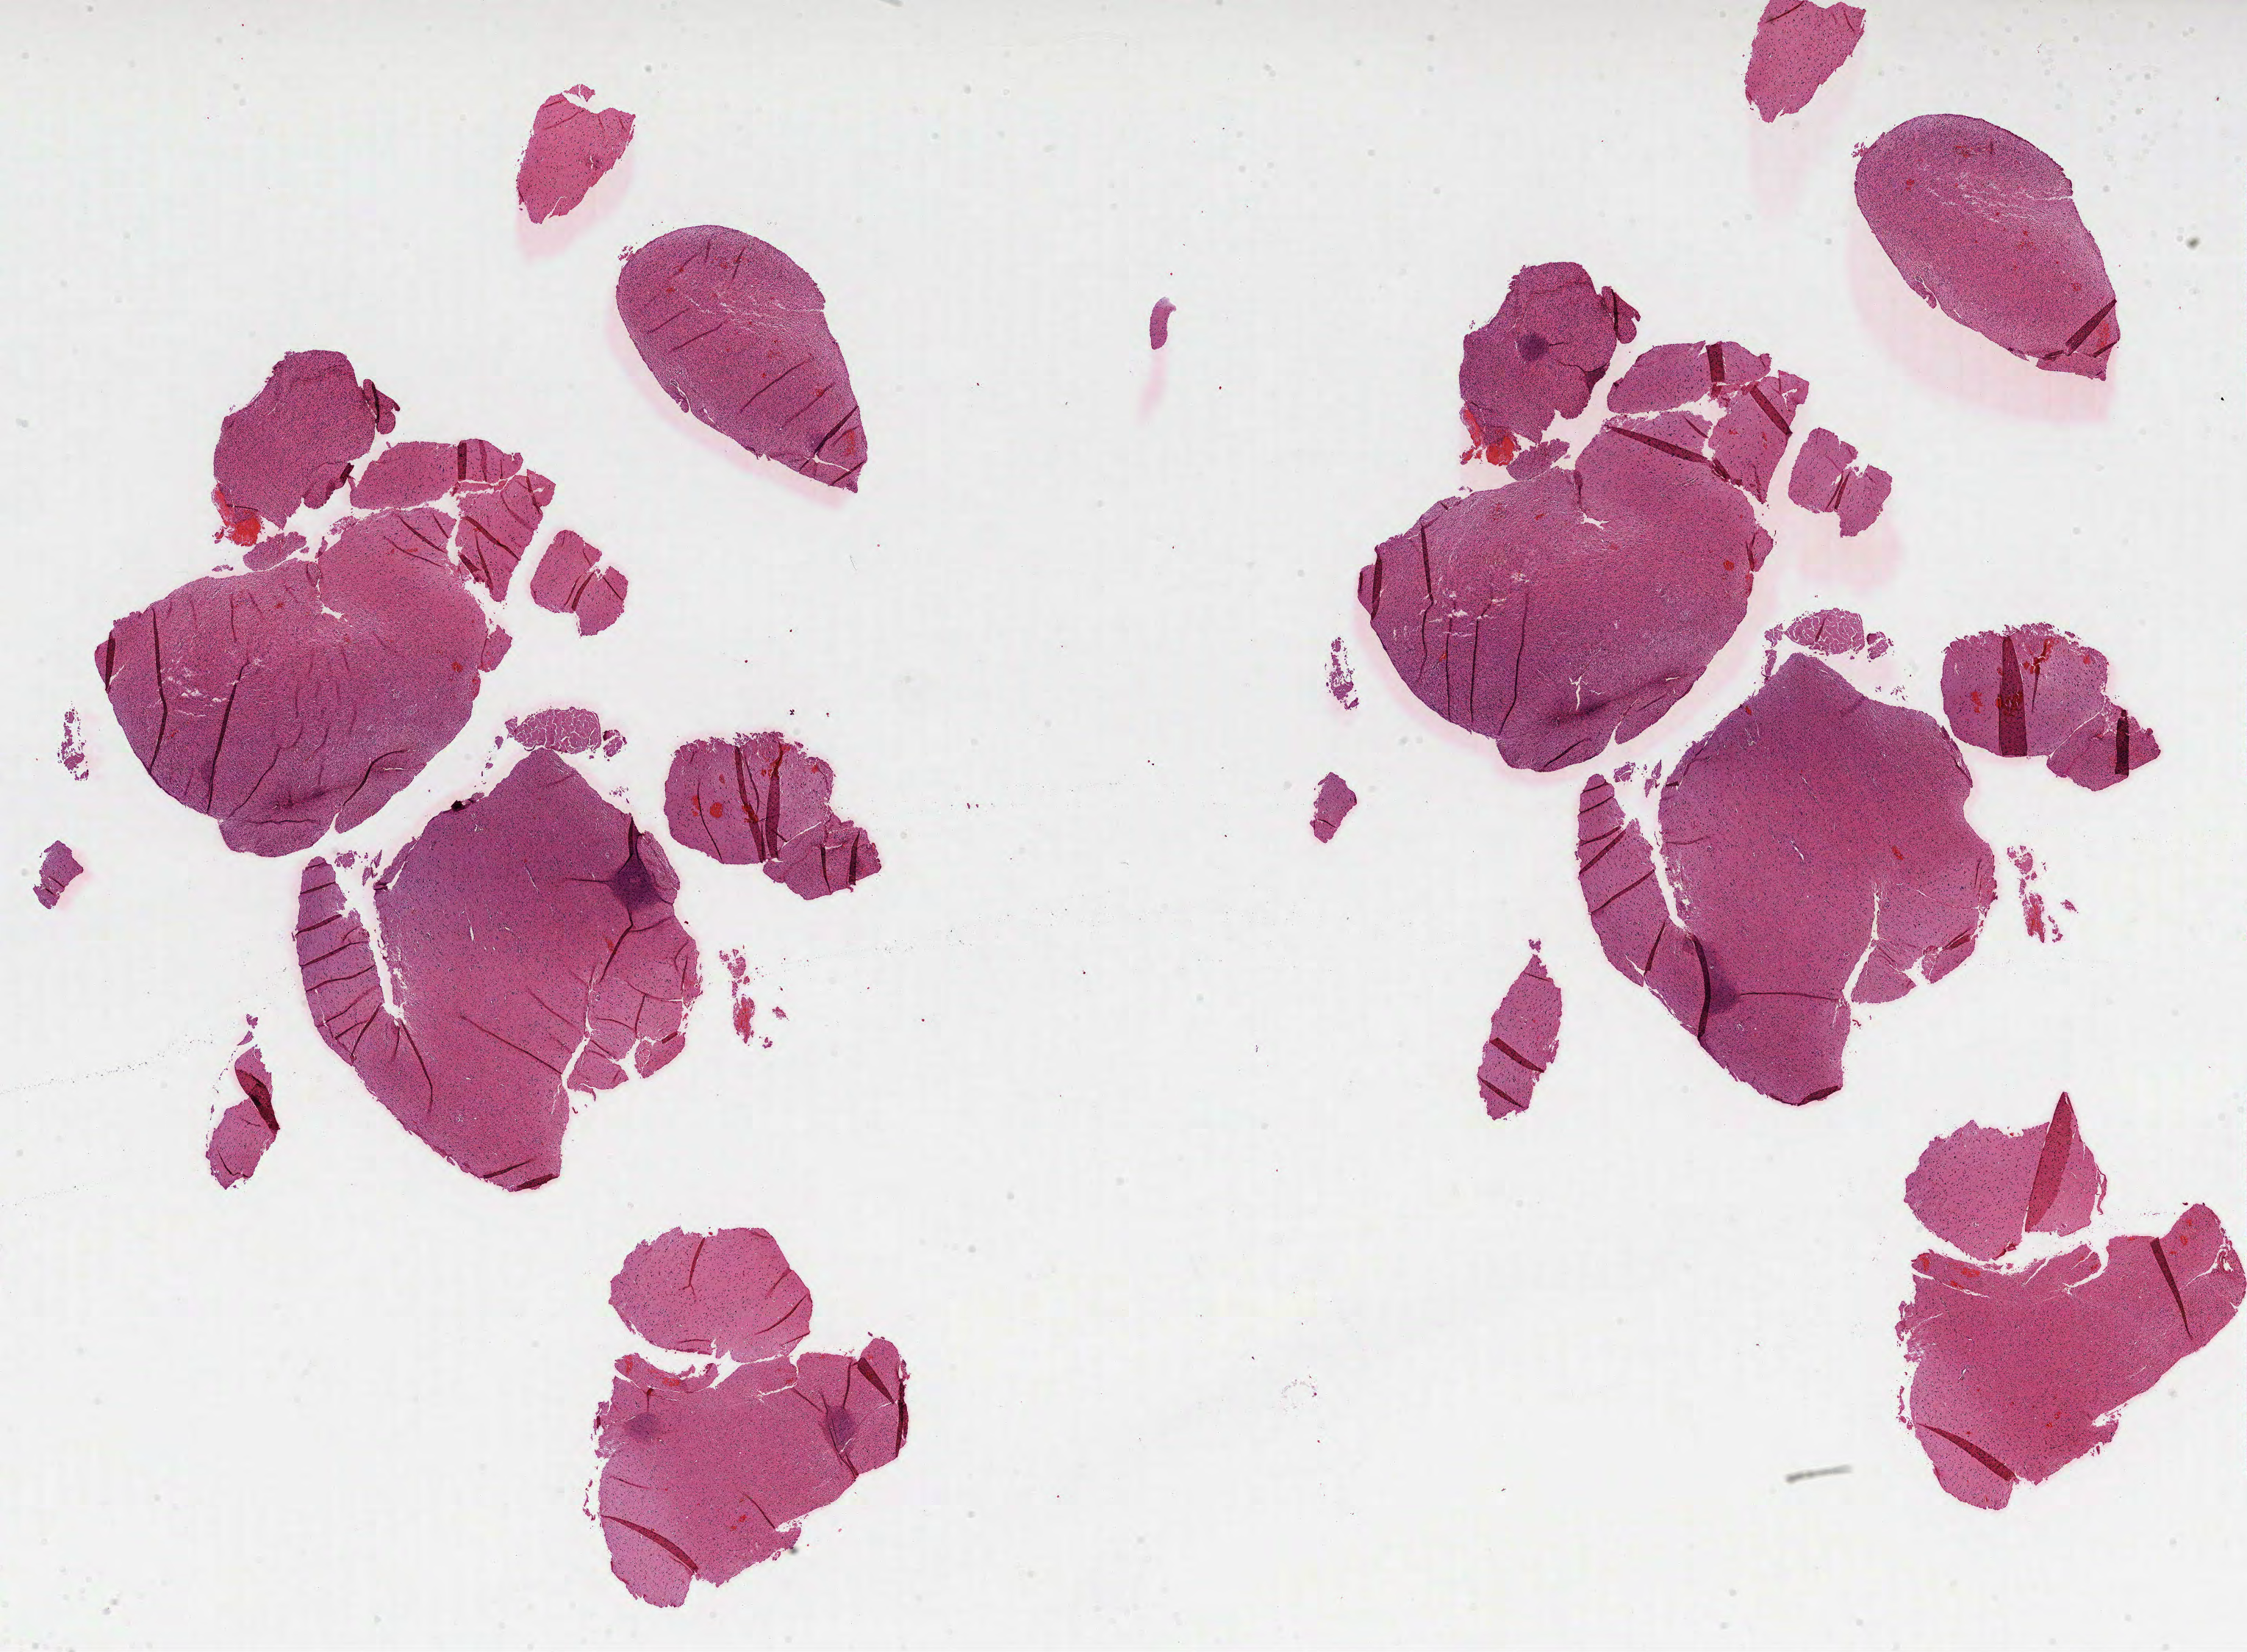
Whole-slide histology image, H&E-stained, shown as a low-resolution overview of the whole scanned area (about 24.7 x 18.1 mm, slide scanned at 40x), formalin-fixed paraffin-embedded (FFPE) diagnostic section, primary tumour sample from the brain. Patient: female, age at initial diagnosis 54 years. Histologic grade: G3 (poorly differentiated).
Diagnosis: Astrocytoma, anaplastic.